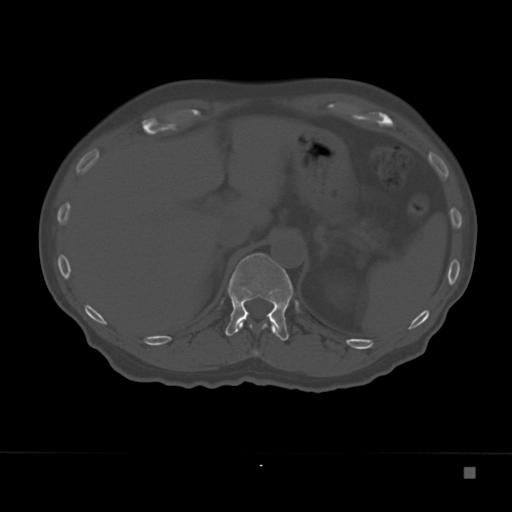
CT including the spine, one axial slice. Slice 139 of 332 in the series (ordered by position). Reconstruction kernel Br40s. 120 kVp. Bone window (W 1800 / L 400 HU). 1.5 mm slice thickness. 512 × 512 image matrix, field of view 389 × 389 mm. Male patient, age 72 years. From the clinical record (not read from this slice): primary cancer: skeletal.
Structures marked on this image (semi-automatic segmentation, software-assisted and operator-edited):
- T11 vertebra: bounding box [x1, y1, x2, y2] px = [239, 323, 276, 356]
- T12 vertebra: [225, 253, 293, 341]